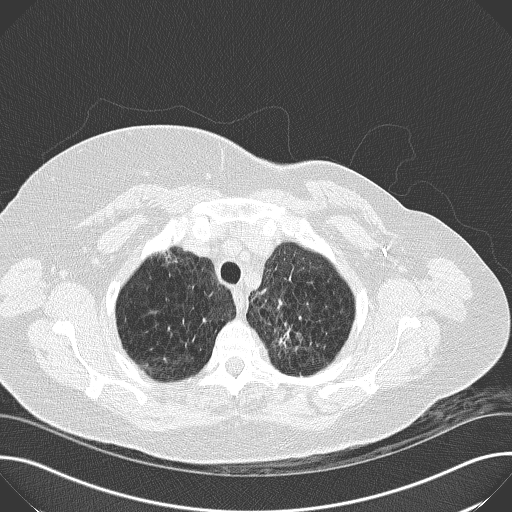
Low-dose screening chest CT, one axial slice. Slice 144 of 169 in the series (ordered by position). 120 kVp. Lung window (W 1500 / L -600 HU). 2 mm slice thickness. 512 × 512 image matrix, field of view 380 × 380 mm.
Outlined on this slice (expert manual segmentation):
- lesion 1 (tumor, upper lobe of left lung): bounding box (x1, y1, x2, y2) in pixels: (278, 329, 298, 349)